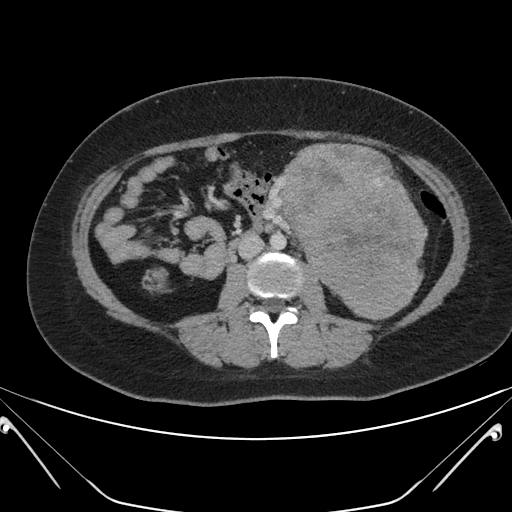
Contrast-enhanced abdominal CT, one axial slice; position 96 of 168 along the scan axis; 120 kVp; intravenous contrast given; soft-tissue window (W 400 / L 40 HU); 3 mm slice thickness; 512 × 512 image matrix. Female patient, age 26 years. Case-level facts recorded for this patient, not image findings: diagnosis: adrenocortical carcinoma; tumour side: left adrenal; tumour size at pathology: 28 cm; Ki-67 index: 20 %; stage (as recorded): 2.
Structures marked on this image (semi-automatically segmented with operator editing):
- mass: box from (x=284, y=145) to (x=425, y=315) px